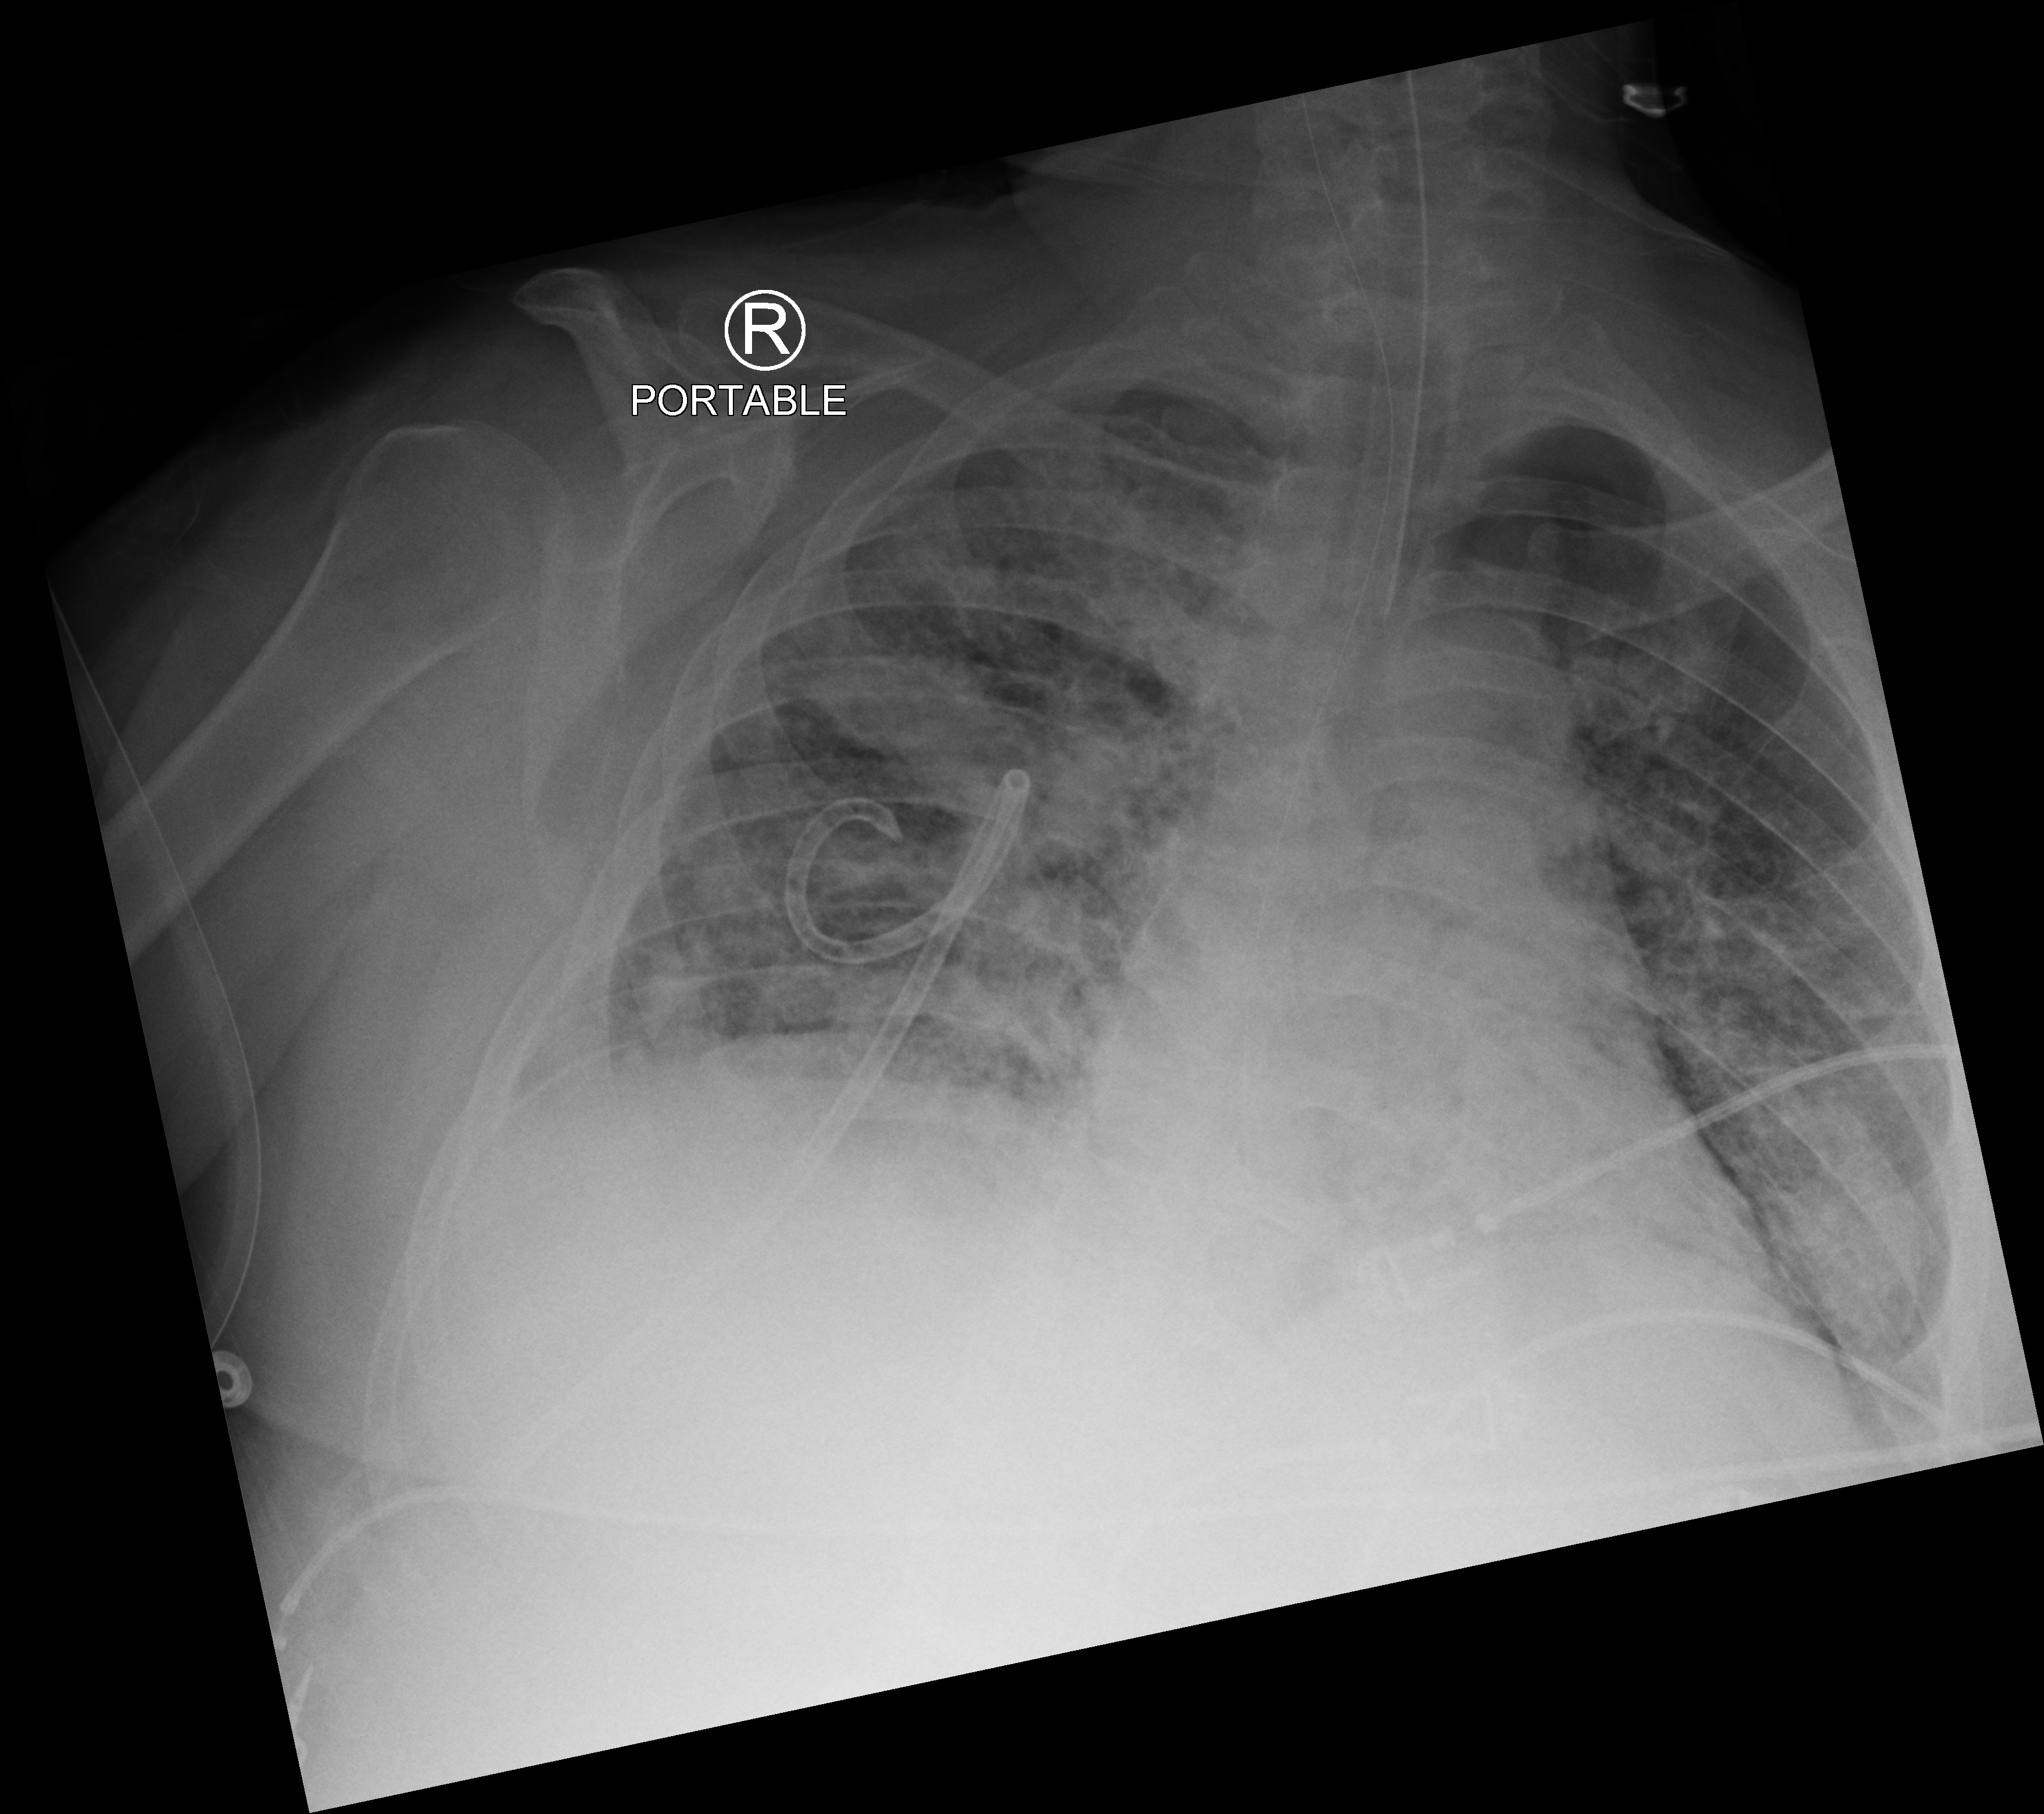
Chest X-ray (portable), anteroposterior (AP) projection. Adult patient hospitalised with COVID-19, age 18–59 years.
From the hospital-stay record, not from the radiograph (when in the stay this image was taken is not recorded):
- mechanically ventilated during this hospital stay: yes
- admitted to intensive care during this hospital stay: yes